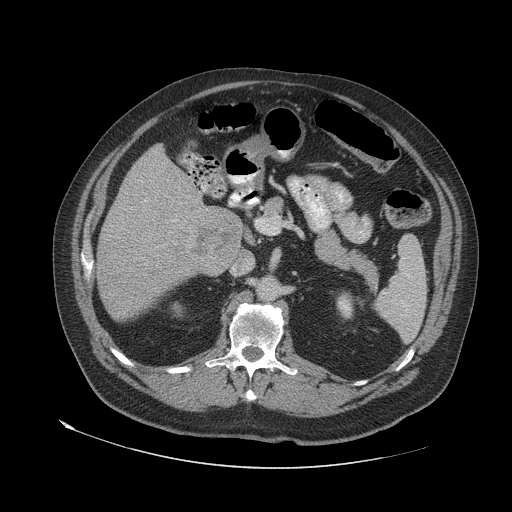
Contrast-enhanced abdominal CT (liver protocol), one axial slice; position 28 of 79 along the scan axis; reconstruction kernel STANDARD; 140 kVp; soft-tissue window (W 400 / L 40 HU); 2.5 mm slice thickness; 512 × 512 image matrix. Case-level facts recorded for this patient, not image findings: diagnosis: hepatocellular carcinoma (patient treated with transarterial chemoembolisation; whether this scan precedes or follows treatment is not stated here); TNM stage (as recorded): Stage-IVA; Child-Pugh class: A; tumour differentiation: well differentiated; tumour nodularity: multinodular.
Annotated regions visible in this slice (semi-automatic segmentation, software-assisted and operator-edited):
- liver parenchyma outside the tumour (the mass and vessels are separate outlines, so this box may not span the whole liver): bounding box [x1, y1, x2, y2] px = [98, 144, 240, 318]